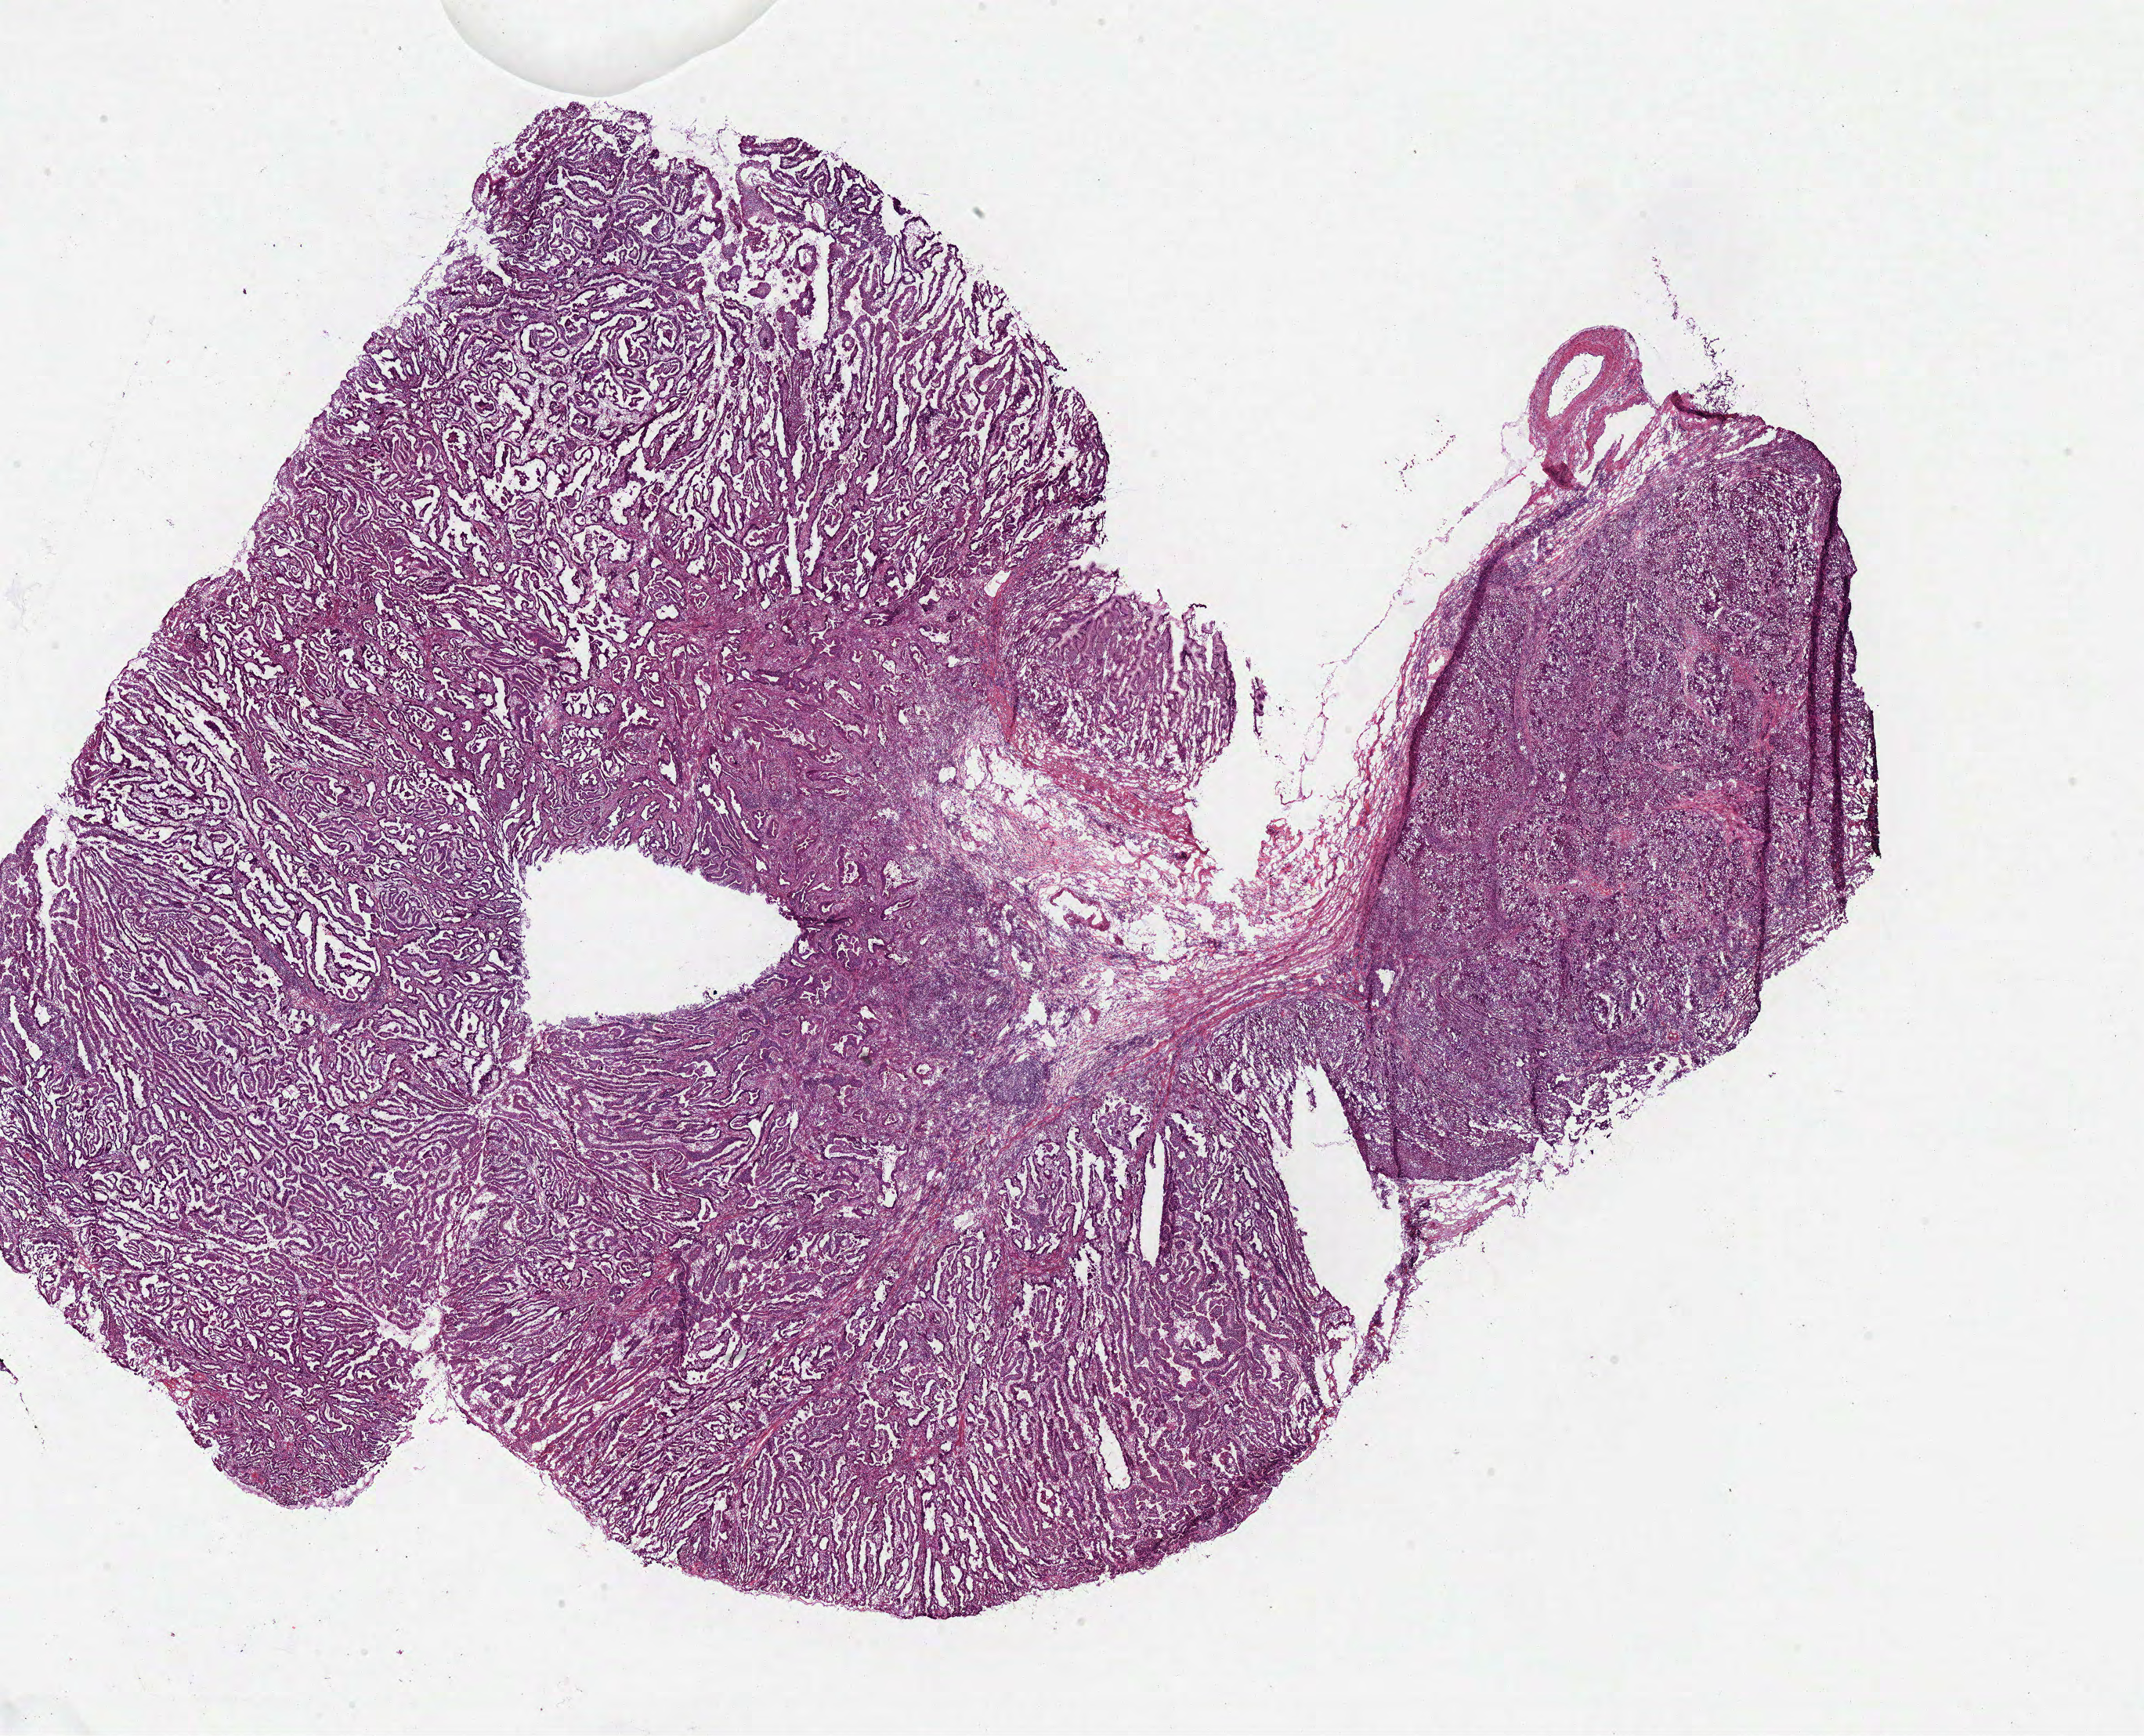
H&E whole-slide image — shown as a low-resolution overview of the whole scanned area (about 21.6 x 17.5 mm, from a 40x scan), frozen section from the bottom of the tissue portion, sample: primary tumour, stomach. Patient: female, age at initial diagnosis 78 years. Histologic grade: G3 (poorly differentiated). Pathologist review of this section (percent, as recorded): tumour cells 95%, tumour nuclei 80%, normal cells 0%, stromal cells 5%, necrosis 0%. Inflammatory infiltration, as recorded: lymphocyte infiltration 5%, monocyte infiltration 0%, neutrophil infiltration 2%.
- AJCC pathologic stage: IIA (7th edition)
- histologic diagnosis: Adenocarcinoma, NOS (body of stomach)
- TNM: T3 N0 M0